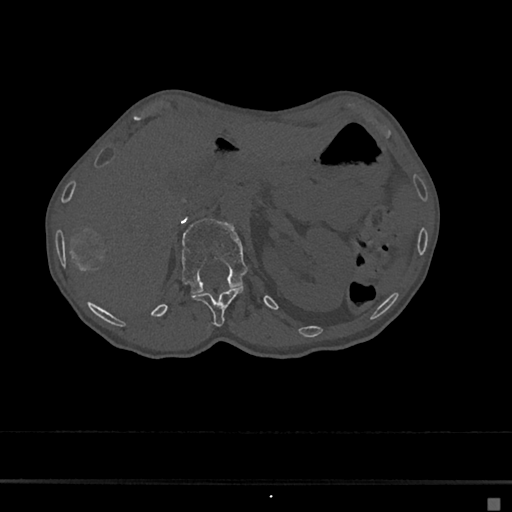
CT including the spine, one axial slice; slice 87 of 797 in the series (ordered by position); reconstruction kernel Br40s/3; bone window (W 1800 / L 400 HU); 512 × 512 image matrix, field of view 360 × 360 mm. Female patient, age 68 years. Case-level facts recorded for this patient, not image findings: primary cancer: renal.
Annotated regions visible in this slice (semi-automatic segmentation, software-assisted and operator-edited):
- L1 vertebra: bounding box <181,219,248,294> (left, top, right, bottom; pixels)
- T12 vertebra: <192,287,244,327>